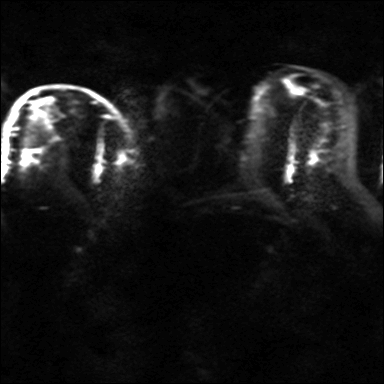
Breast MRI, one axial slice. Position 19 of 36 along the scan axis. Diffusion-weighted series; image 2 of 4 stored at this slice position (different b-values; order by instance number). 3 T. 4 mm slice thickness. 384 × 384 image matrix, field of view 320 × 320 mm. Female patient.
Structures marked on this image (outlined manually by an expert reader):
- tumour on diffusion-weighted imaging: bounding box <25,151,31,164> (left, top, right, bottom; pixels)